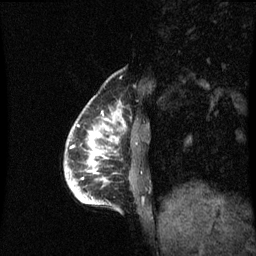
Breast MRI (dynamic contrast-enhanced), one sagittal slice. Dynamic contrast-enhanced series, image 2 of 3 at this slice position (ordered by acquisition). 1.5 T. TE 4.2 ms, TR 8.9 ms. 2 mm slice thickness. 256 × 256 image matrix. Female patient, age 35 years. From the clinical record (not read from this slice): setting: breast cancer imaged before/during neoadjuvant chemotherapy; receptor status: HR-positive, HER2-negative.
Annotated regions visible in this slice (semi-automatic segmentation, software-assisted and operator-edited):
- analysis volume of interest (the breast-tissue region the enhancement analysis was run in; not a lesion): box from (x=66, y=120) to (x=124, y=205) px
- tumour enhancement mask (voxels above the 70 % enhancement threshold inside the analysis volume of interest): (x=83, y=126)–(x=109, y=203)